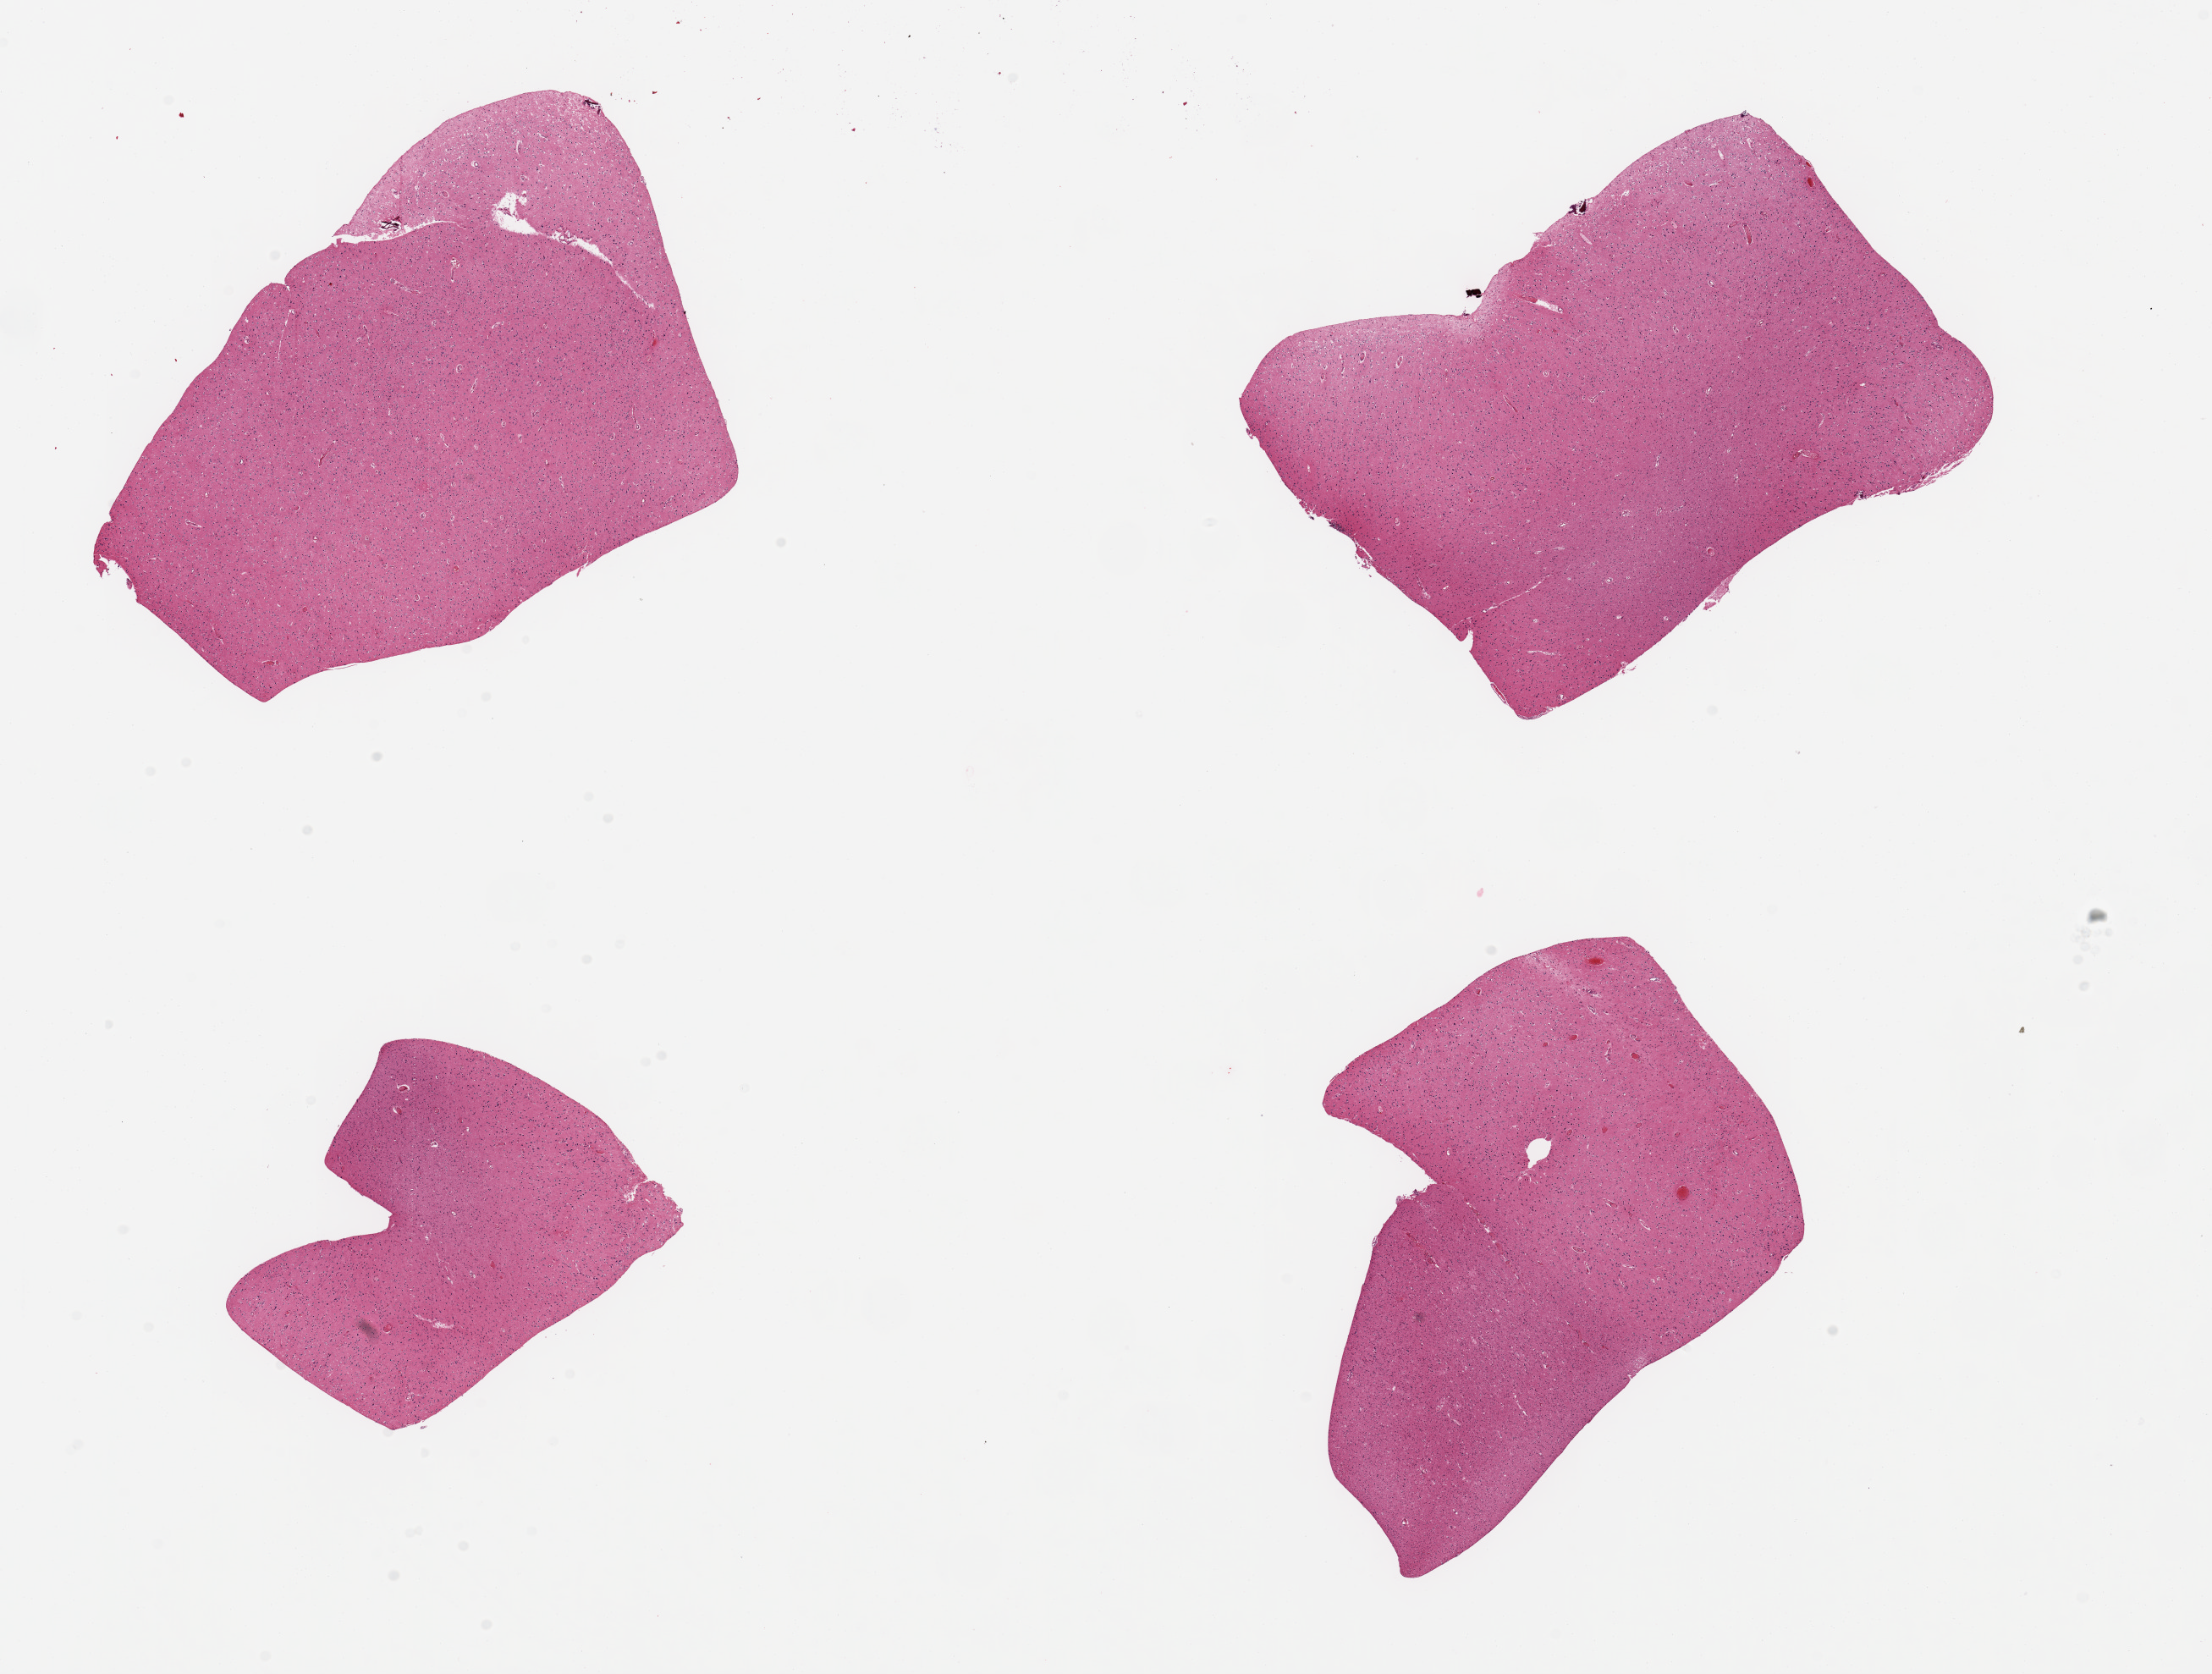
Whole-slide image, haematoxylin and eosin stain, shown as a low-resolution overview of the whole scanned area (about 20.7 x 15.6 mm, from a 20x scan), PAXgene-fixed paraffin-embedded (PFPE) section, target tissue: cerebral cortex, tissue donor sample. Donor: male.
Pathologist's review note for this sample: 4 pieces.